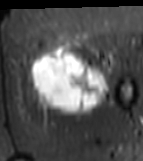
MRI of an extremity soft-tissue mass, one axial slice. Position 22 of 81 along the scan axis. STIR. MR volume resampled by the dataset authors to the PET/CT grid (not the native acquisition matrix). 3.27 mm slice thickness. 143 × 161 image matrix. Female patient. From the clinical record (not read from this slice): histological type: myxofibrosarcoma; grade: intermediate; site of the primary tumour: left thigh.
Structures marked on this image (expert contour drawn on MRI and transferred to this co-registered scan by the dataset authors):
- gross tumour volume including surrounding oedema: box from (x=28, y=42) to (x=114, y=116) px
- gross tumour volume (mass): (x=31, y=47)–(x=112, y=112)